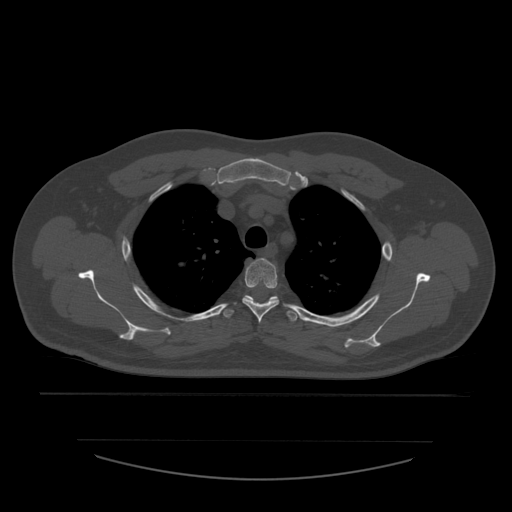
CT including the spine, one axial slice; position 431 of 532 along the scan axis; reconstruction kernel STANDARD; bone window (W 1800 / L 400 HU); 1.25 mm slice thickness; 512 × 512 image matrix, field of view 441 × 441 mm. Patient age 44 years. From the clinical record (not read from this slice): primary cancer: soft tissue sarcoma.
Outlined on this slice (semi-automatic segmentation, software-assisted and operator-edited):
- T3 vertebra: box from (x=242, y=258) to (x=280, y=323) px
- T4 vertebra: (x=224, y=296)–(x=298, y=322)